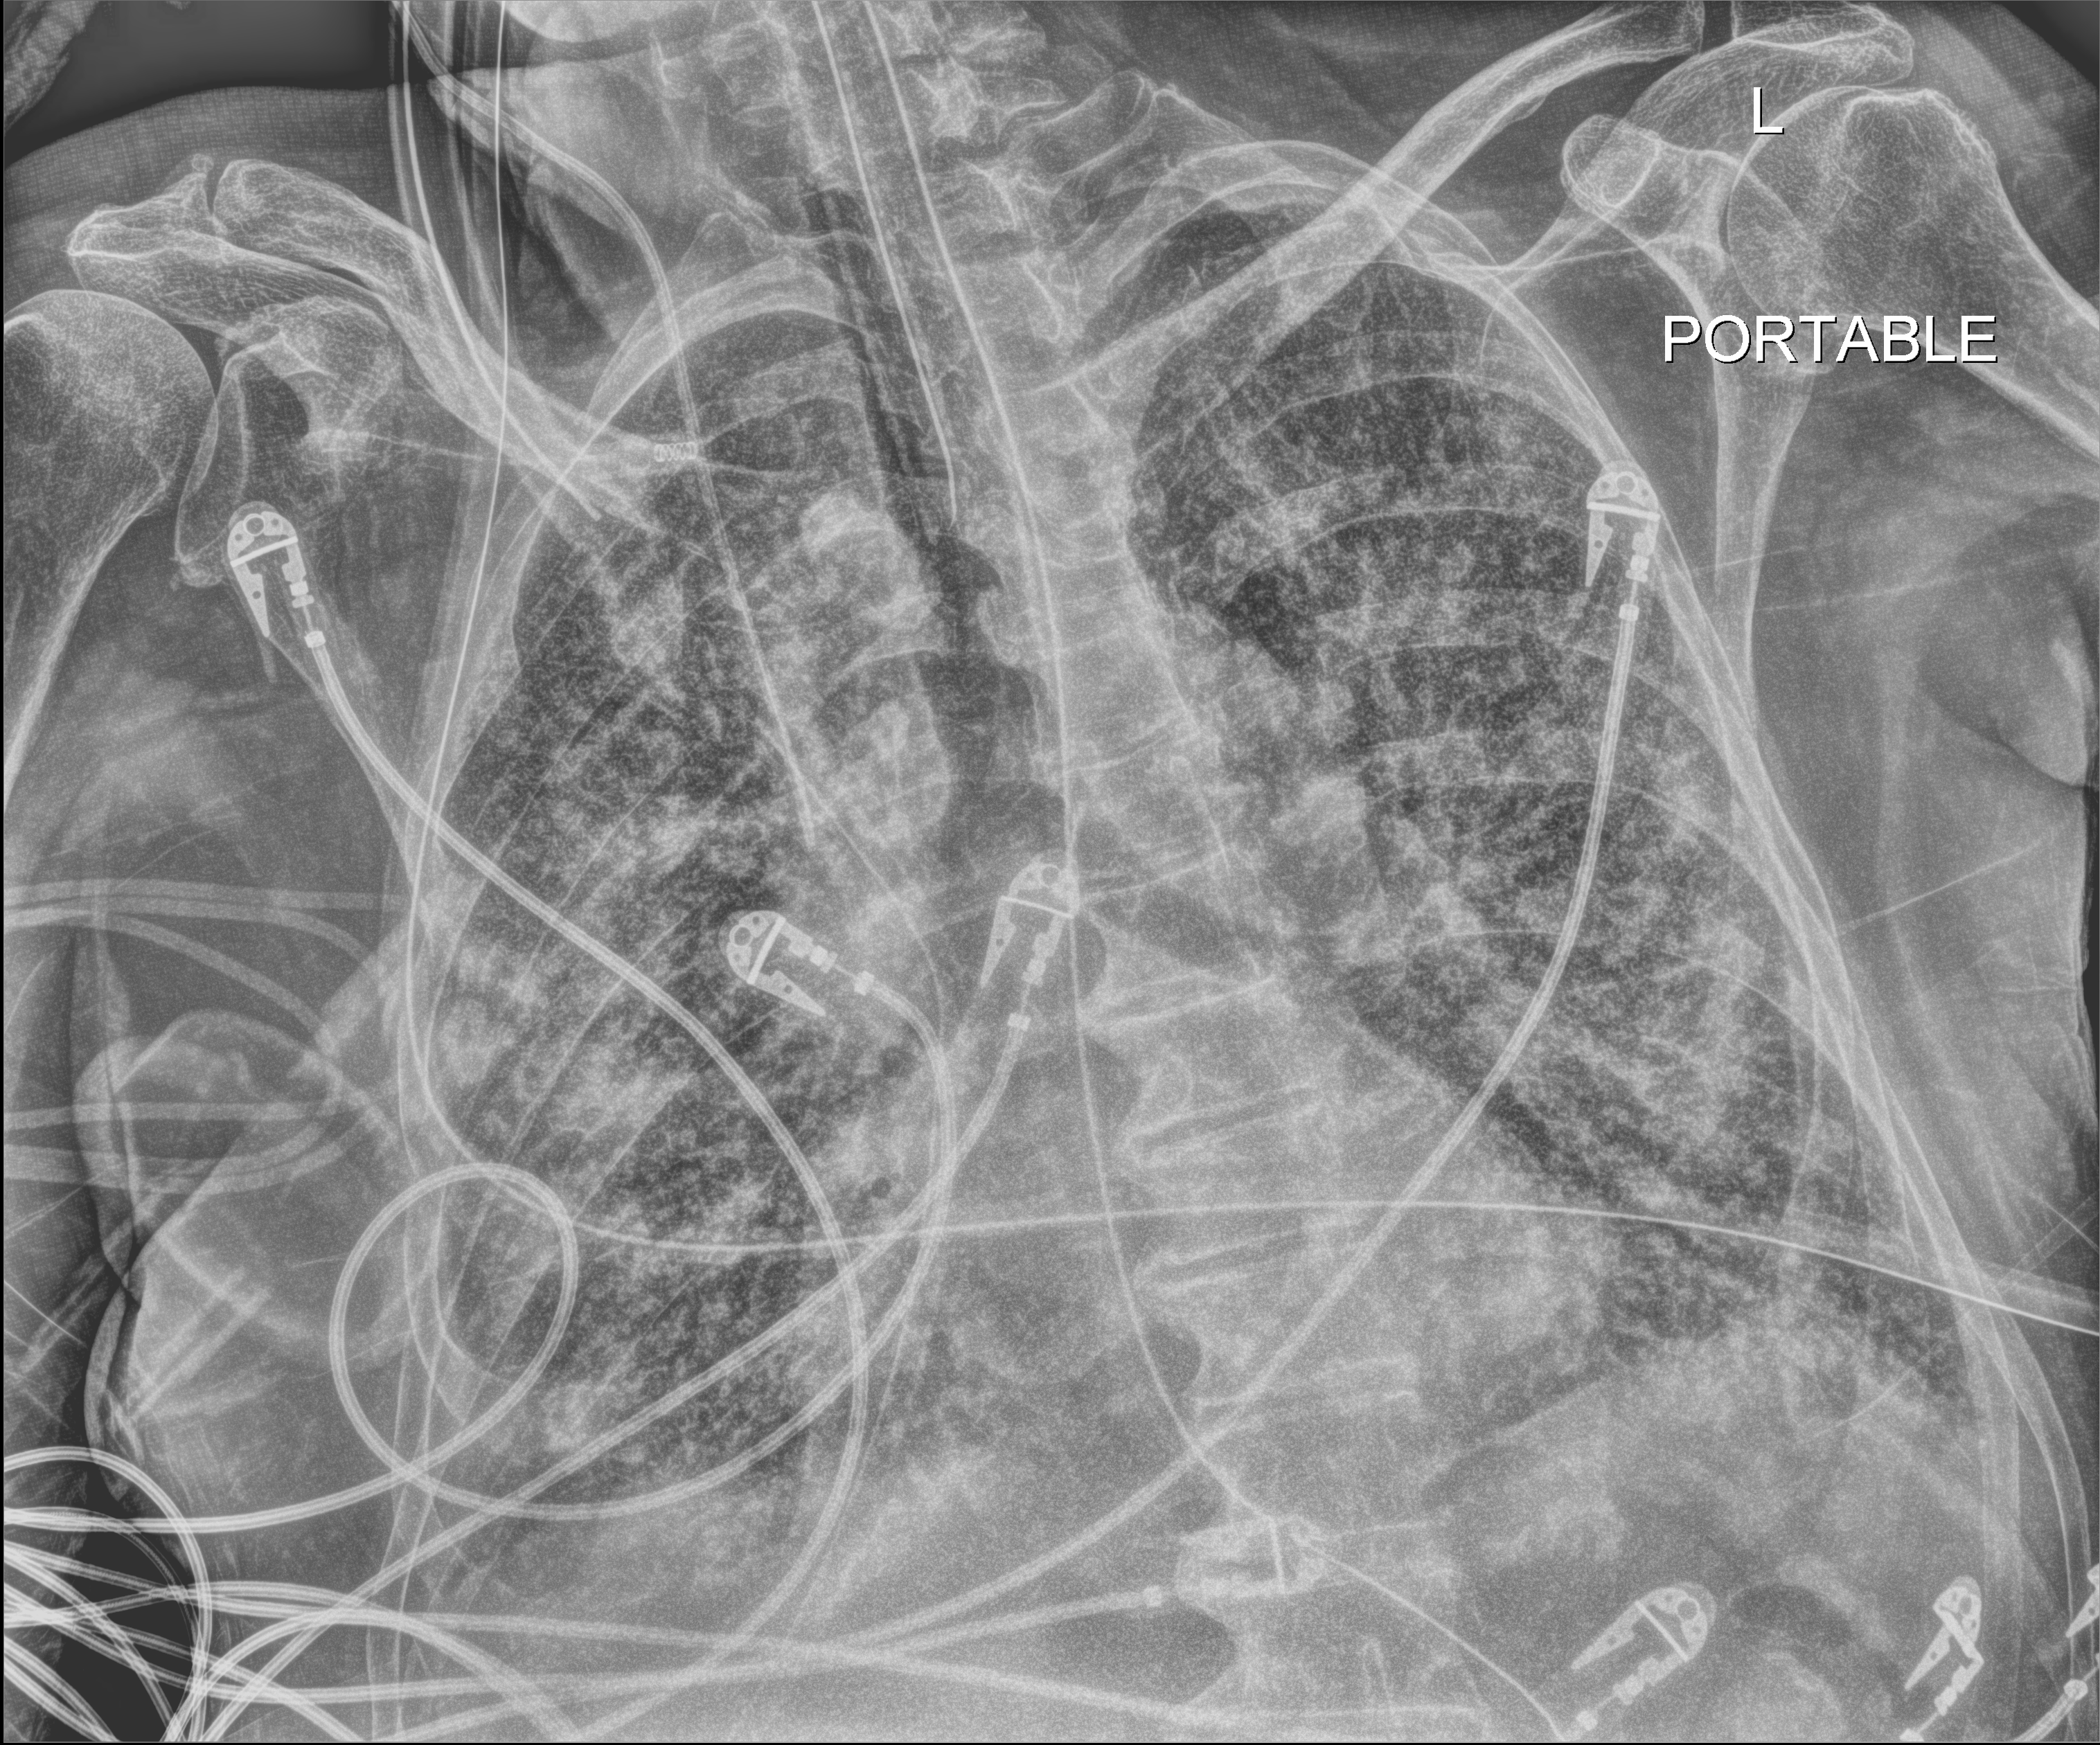
Chest X-ray (portable); anteroposterior (AP) projection. Patient hospitalised with COVID-19; male, aged 75–90 years.
Hospital-stay facts (about this admission, not read from this image; timing relative to this image not recorded): length of hospital stay: 47 days; admitted to intensive care during this hospital stay: yes.